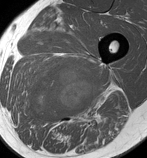
MRI of an extremity soft-tissue mass, one axial slice; position 76 of 86 along the scan axis; MR volume resampled by the dataset authors to the PET/CT grid (not the native acquisition matrix); 3.27 mm slice thickness; 147 × 158 image matrix, field of view 144 × 154 mm. Male patient. From the clinical record (not read from this slice): histological type: undifferentiated pleomorphic liposarcoma; grade: high; site of the primary tumour: left thigh.
Structures marked on this image (expert contour drawn on MRI and transferred to this co-registered scan by the dataset authors):
- gross tumour volume including surrounding oedema: bounding box [x1, y1, x2, y2] px = [23, 63, 106, 125]
- gross tumour volume (mass): [28, 65, 97, 121]